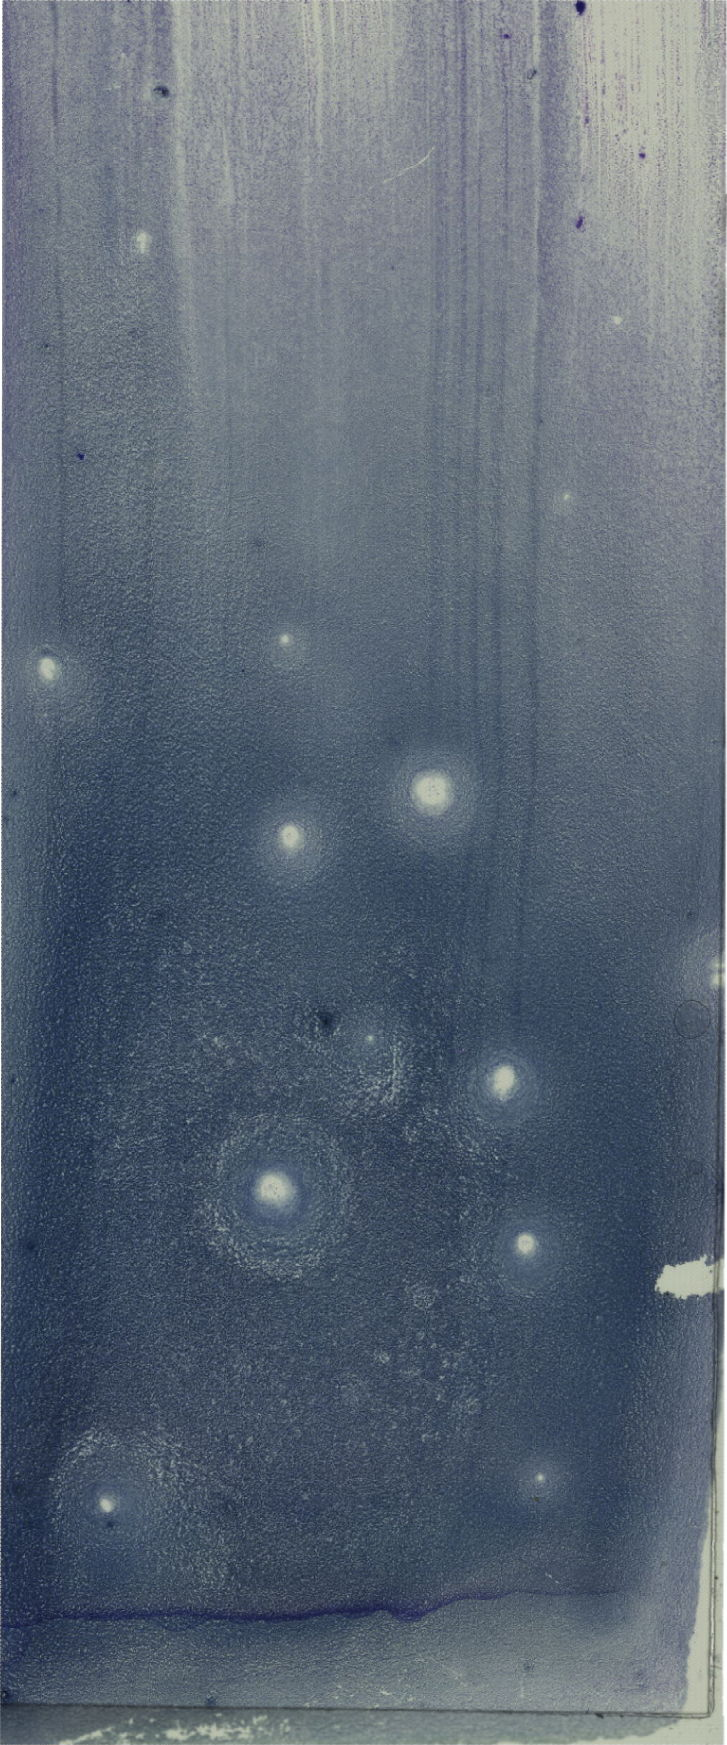
Whole-slide image of a May-Grünwald-Giemsa (MGG)-stained bone marrow aspirate smear, shown as a low-resolution overview of the whole scanned area (about 20.6 x 49.5 mm). Patient sex: male.
Diagnosis: B Acute Lymphoblastic Leukemia.